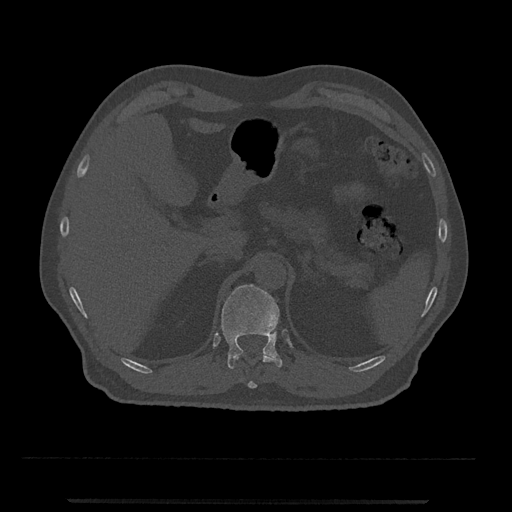
CT including the spine, one axial slice. Slice 426 of 797 in the series (ordered by position). Reconstruction kernel Br40s/3. Bone window (W 1800 / L 400 HU). 0.5 mm slice thickness. 512 × 512 image matrix. Male patient, age 63 years. Case-level facts recorded for this patient, not image findings: primary cancer: prostate.
Structures marked on this image (semi-automatic segmentation, software-assisted and operator-edited):
- T11 vertebra: bounding box <235,352,273,388> (left, top, right, bottom; pixels)
- T12 vertebra: <221,284,283,369>